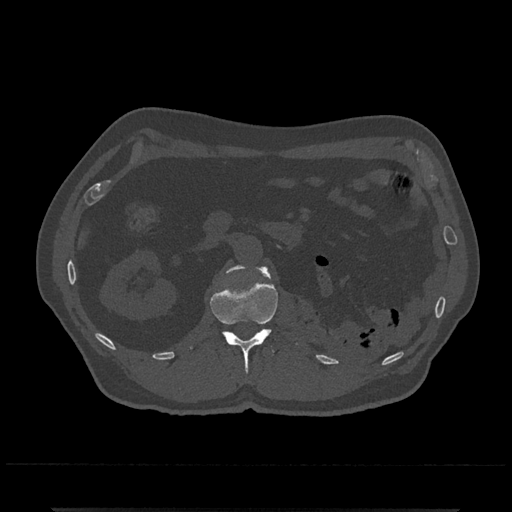
CT including the spine, one axial slice; slice 351 of 797 in the series (ordered by position); reconstruction kernel Br40s/3; 120 kVp; bone window (W 1800 / L 400 HU); 512 × 512 image matrix, field of view 393 × 393 mm. Patient: male, 67 years. Case-level facts recorded for this patient, not image findings: primary cancer: prostate.
Annotated regions visible in this slice (semi-automatic segmentation, software-assisted and operator-edited):
- L1 vertebra: bounding box (x1, y1, x2, y2) in pixels: (190, 265, 278, 374)